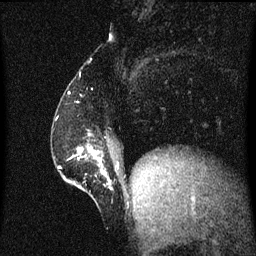
Breast MRI (dynamic contrast-enhanced), one sagittal slice. Slice 17 of 60 in the series (ordered by position). Dynamic contrast-enhanced series, image 2 of 3 at this slice position (ordered by acquisition). 1.5 T. TE 4.2 ms, TR 8.4 ms. 2 mm slice thickness. 256 × 256 image matrix, field of view 200 × 200 mm. Patient: female, 52 years. Case-level facts recorded for this patient, not image findings: setting: breast cancer imaged before/during neoadjuvant chemotherapy; receptor status: HER2-positive.
Annotated regions visible in this slice (semi-automatically segmented with operator editing):
- analysis volume of interest (the breast-tissue region the enhancement analysis was run in; not a lesion): box from (x=62, y=132) to (x=114, y=197) px
- tumour enhancement mask (voxels above the 70 % enhancement threshold inside the analysis volume of interest): (x=78, y=148)–(x=107, y=175)